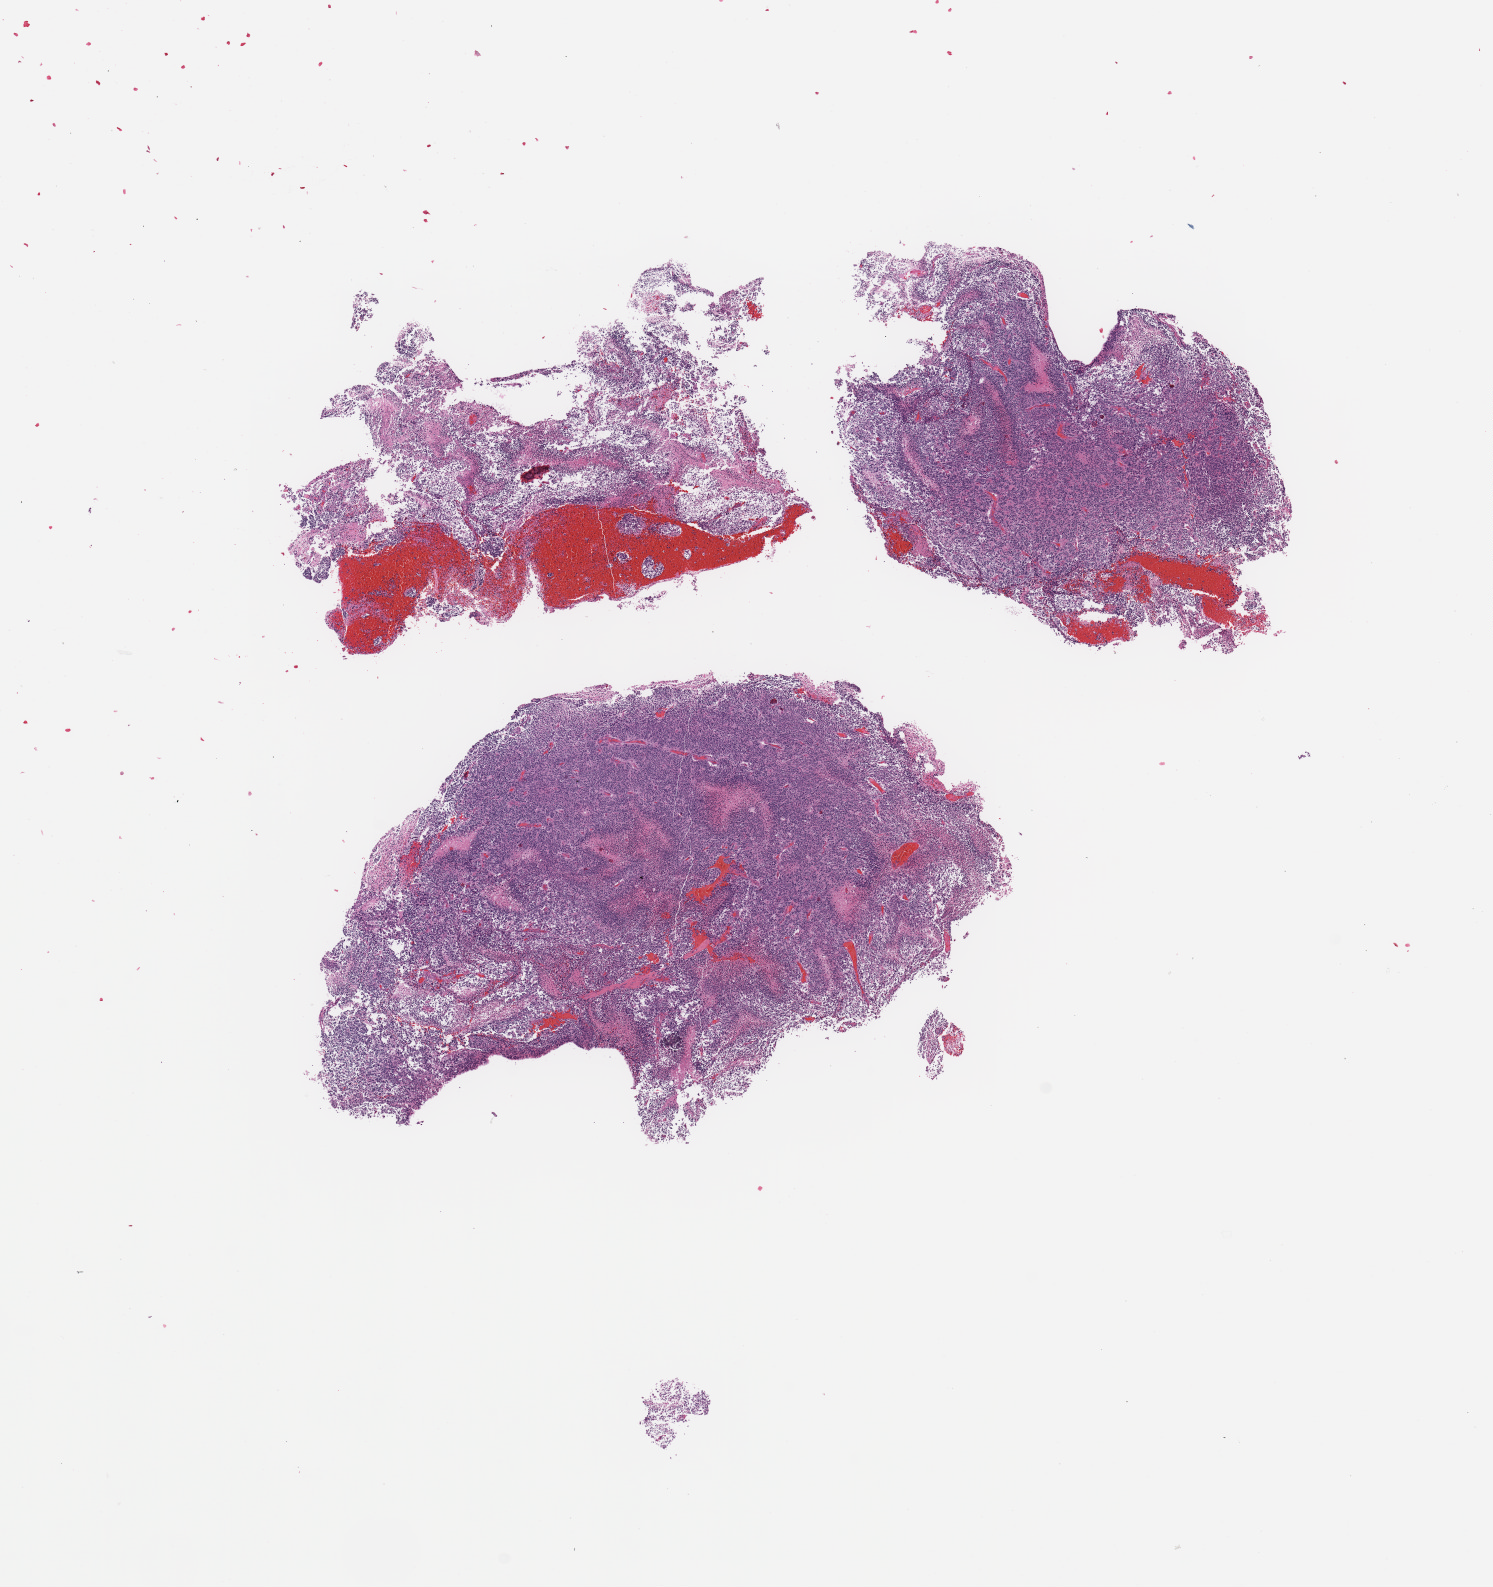
Digitized Hematoxylin and eosin (H&E) stained tissue section (whole slide) — low-resolution overview of the scanned area, about 11.8 x 12.6 mm, brain, tumour tissue. 48-year-old male patient.
• diagnosis: Glioblastoma